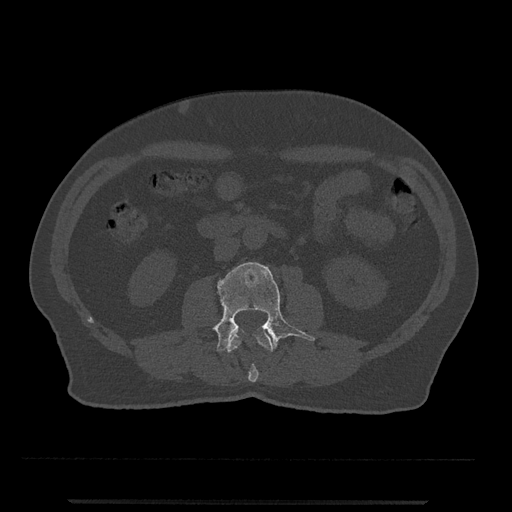
CT including the spine, one axial slice; slice 218 of 797 in the series (ordered by position); reconstruction kernel Br40s/3; bone window (W 1800 / L 400 HU); 0.5 mm slice thickness; 512 × 512 image matrix, field of view 419 × 419 mm. Patient: male, 63 years. Case-level facts recorded for this patient, not image findings: primary cancer: prostate.
Outlined on this slice (semi-automatic segmentation, software-assisted and operator-edited):
- L2 vertebra: bounding box (x1, y1, x2, y2) in pixels: (227, 332, 273, 382)
- L3 vertebra: (213, 262, 315, 352)